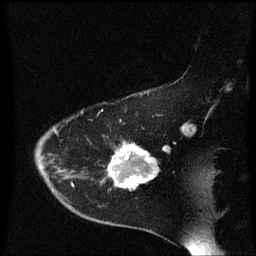
Breast MRI (dynamic contrast-enhanced), one sagittal slice. Slice 45 of 60 in the series (ordered by position). Dynamic contrast-enhanced series, image 2 of 3 at this slice position (ordered by acquisition). 1.5 T. TE 4.2 ms, TR 8.4 ms. 256 × 256 image matrix, field of view 200 × 200 mm. Patient: female, 54 years. From the clinical record (not read from this slice): setting: breast cancer imaged before/during neoadjuvant chemotherapy; receptor status: HR-positive, HER2-negative.
Annotated regions visible in this slice (semi-automatically segmented with operator editing):
- analysis volume of interest (the breast-tissue region the enhancement analysis was run in; not a lesion): bounding box <103,144,159,191> (left, top, right, bottom; pixels)
- tumour enhancement mask (voxels above the 70 % enhancement threshold inside the analysis volume of interest): <110,144,158,189>